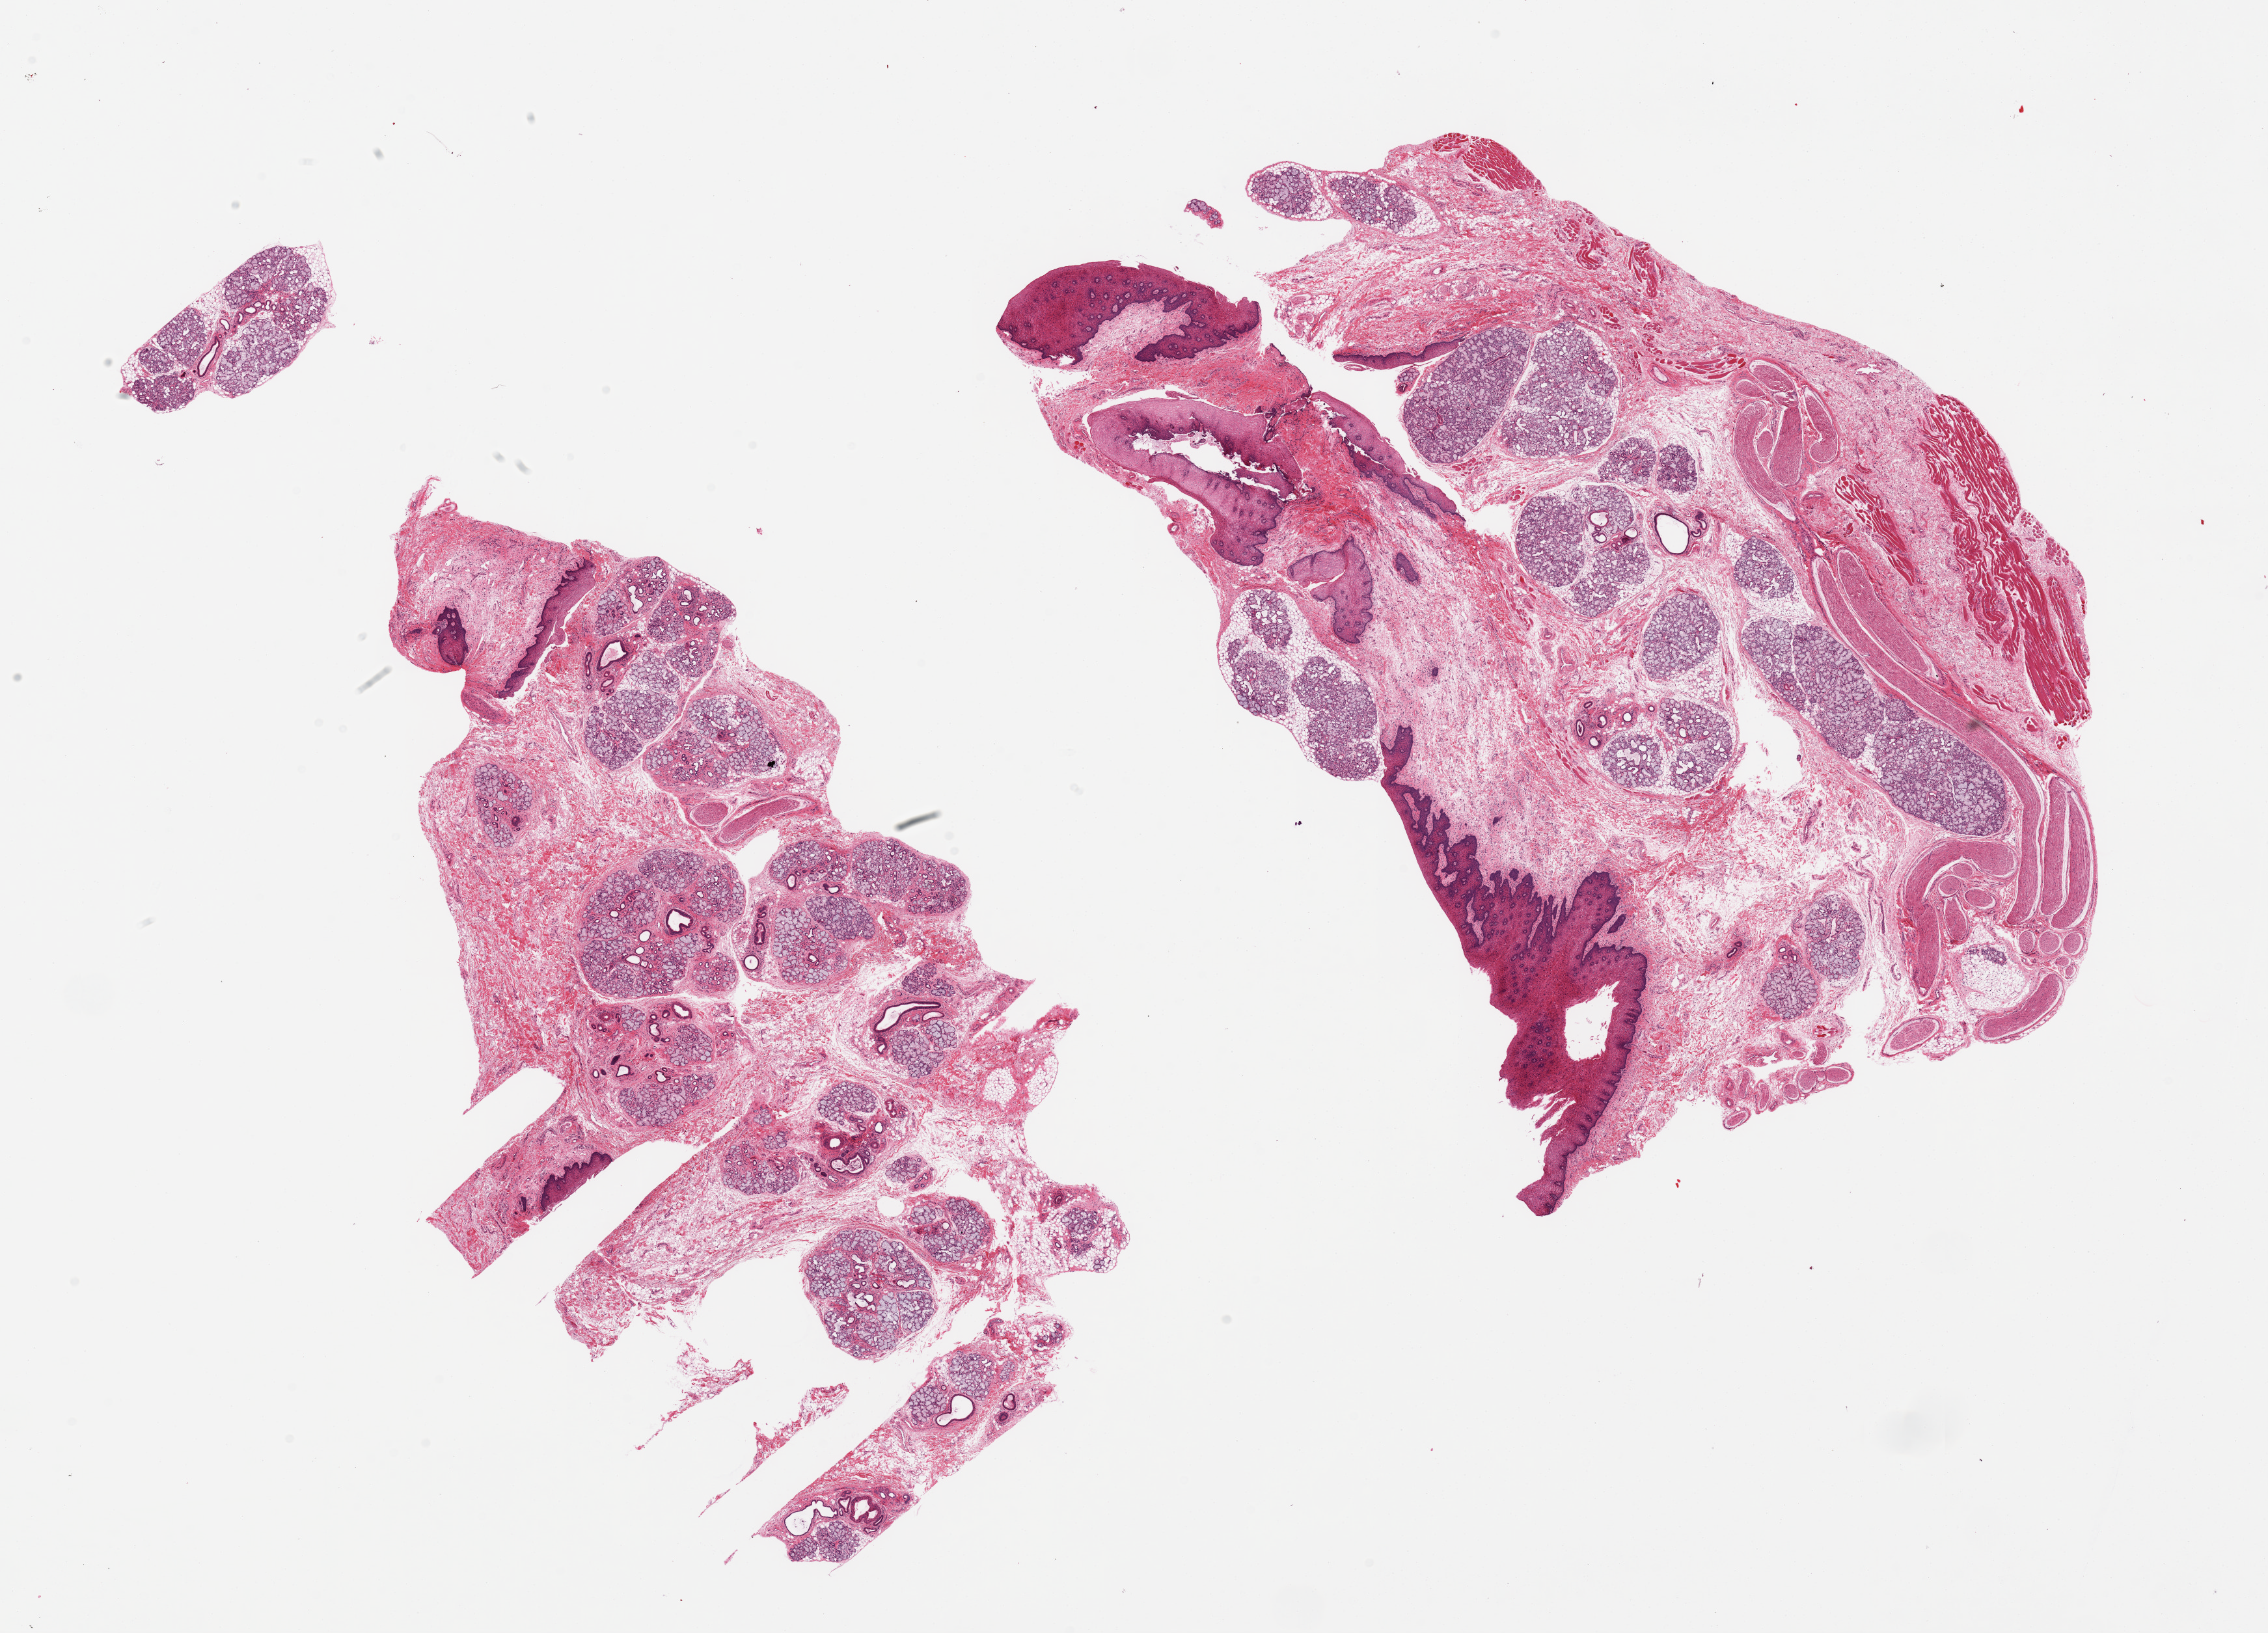
Digitized haematoxylin and eosin-stained section — low-resolution overview of the scanned area, about 27.6 x 19.9 mm, PAXgene-fixed paraffin-embedded (PFPE) section, section of minor salivary gland (target tissue), donor tissue sample. Donor: male.
• pathologist's review note for this sample: 2 pieces,j ~40% glandular tissue, rest is squamous mucosa/muscle/stroma